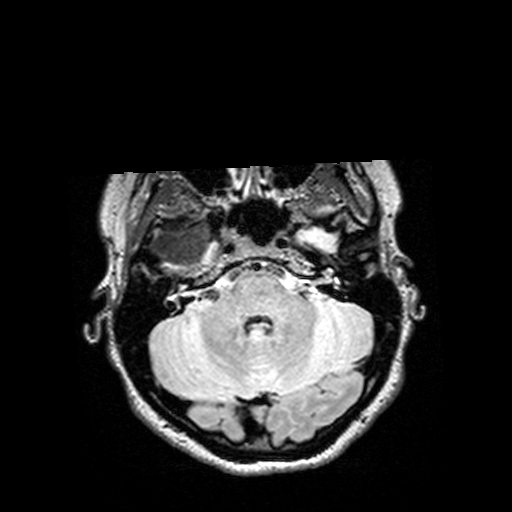
Brain MRI from a brain-tumour surgery series, one axial slice. Slice 109 of 144 in the series (ordered by position). T2 FLAIR. 1 mm slice thickness. 512 × 512 image matrix, field of view 250 × 250 mm. Case-level facts recorded for this patient, not image findings: histopathology: Astrocytoma; WHO grade: 3; IDH mutation: yes.
Annotated regions visible in this slice (outlined manually by an expert reader):
- tumour: bounding box <131,223,191,267> (left, top, right, bottom; pixels)